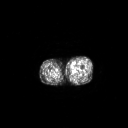
FDG PET of an extremity soft-tissue mass (from a PET/CT study), one axial slice. Slice 233 of 267 in the series (ordered by position). 3.27 mm slice thickness. 128 × 128 image matrix, field of view 700 × 700 mm. Patient: male, 48 years. Case-level facts recorded for this patient, not image findings: histological type: pleiomorphic leiomyosarcoma; grade: high; site of the primary tumour: left thigh.
Structures marked on this image (expert contour drawn on MRI and transferred to this co-registered scan by the dataset authors):
- gross tumour volume including surrounding oedema: bounding box [x1, y1, x2, y2] px = [69, 64, 74, 70]